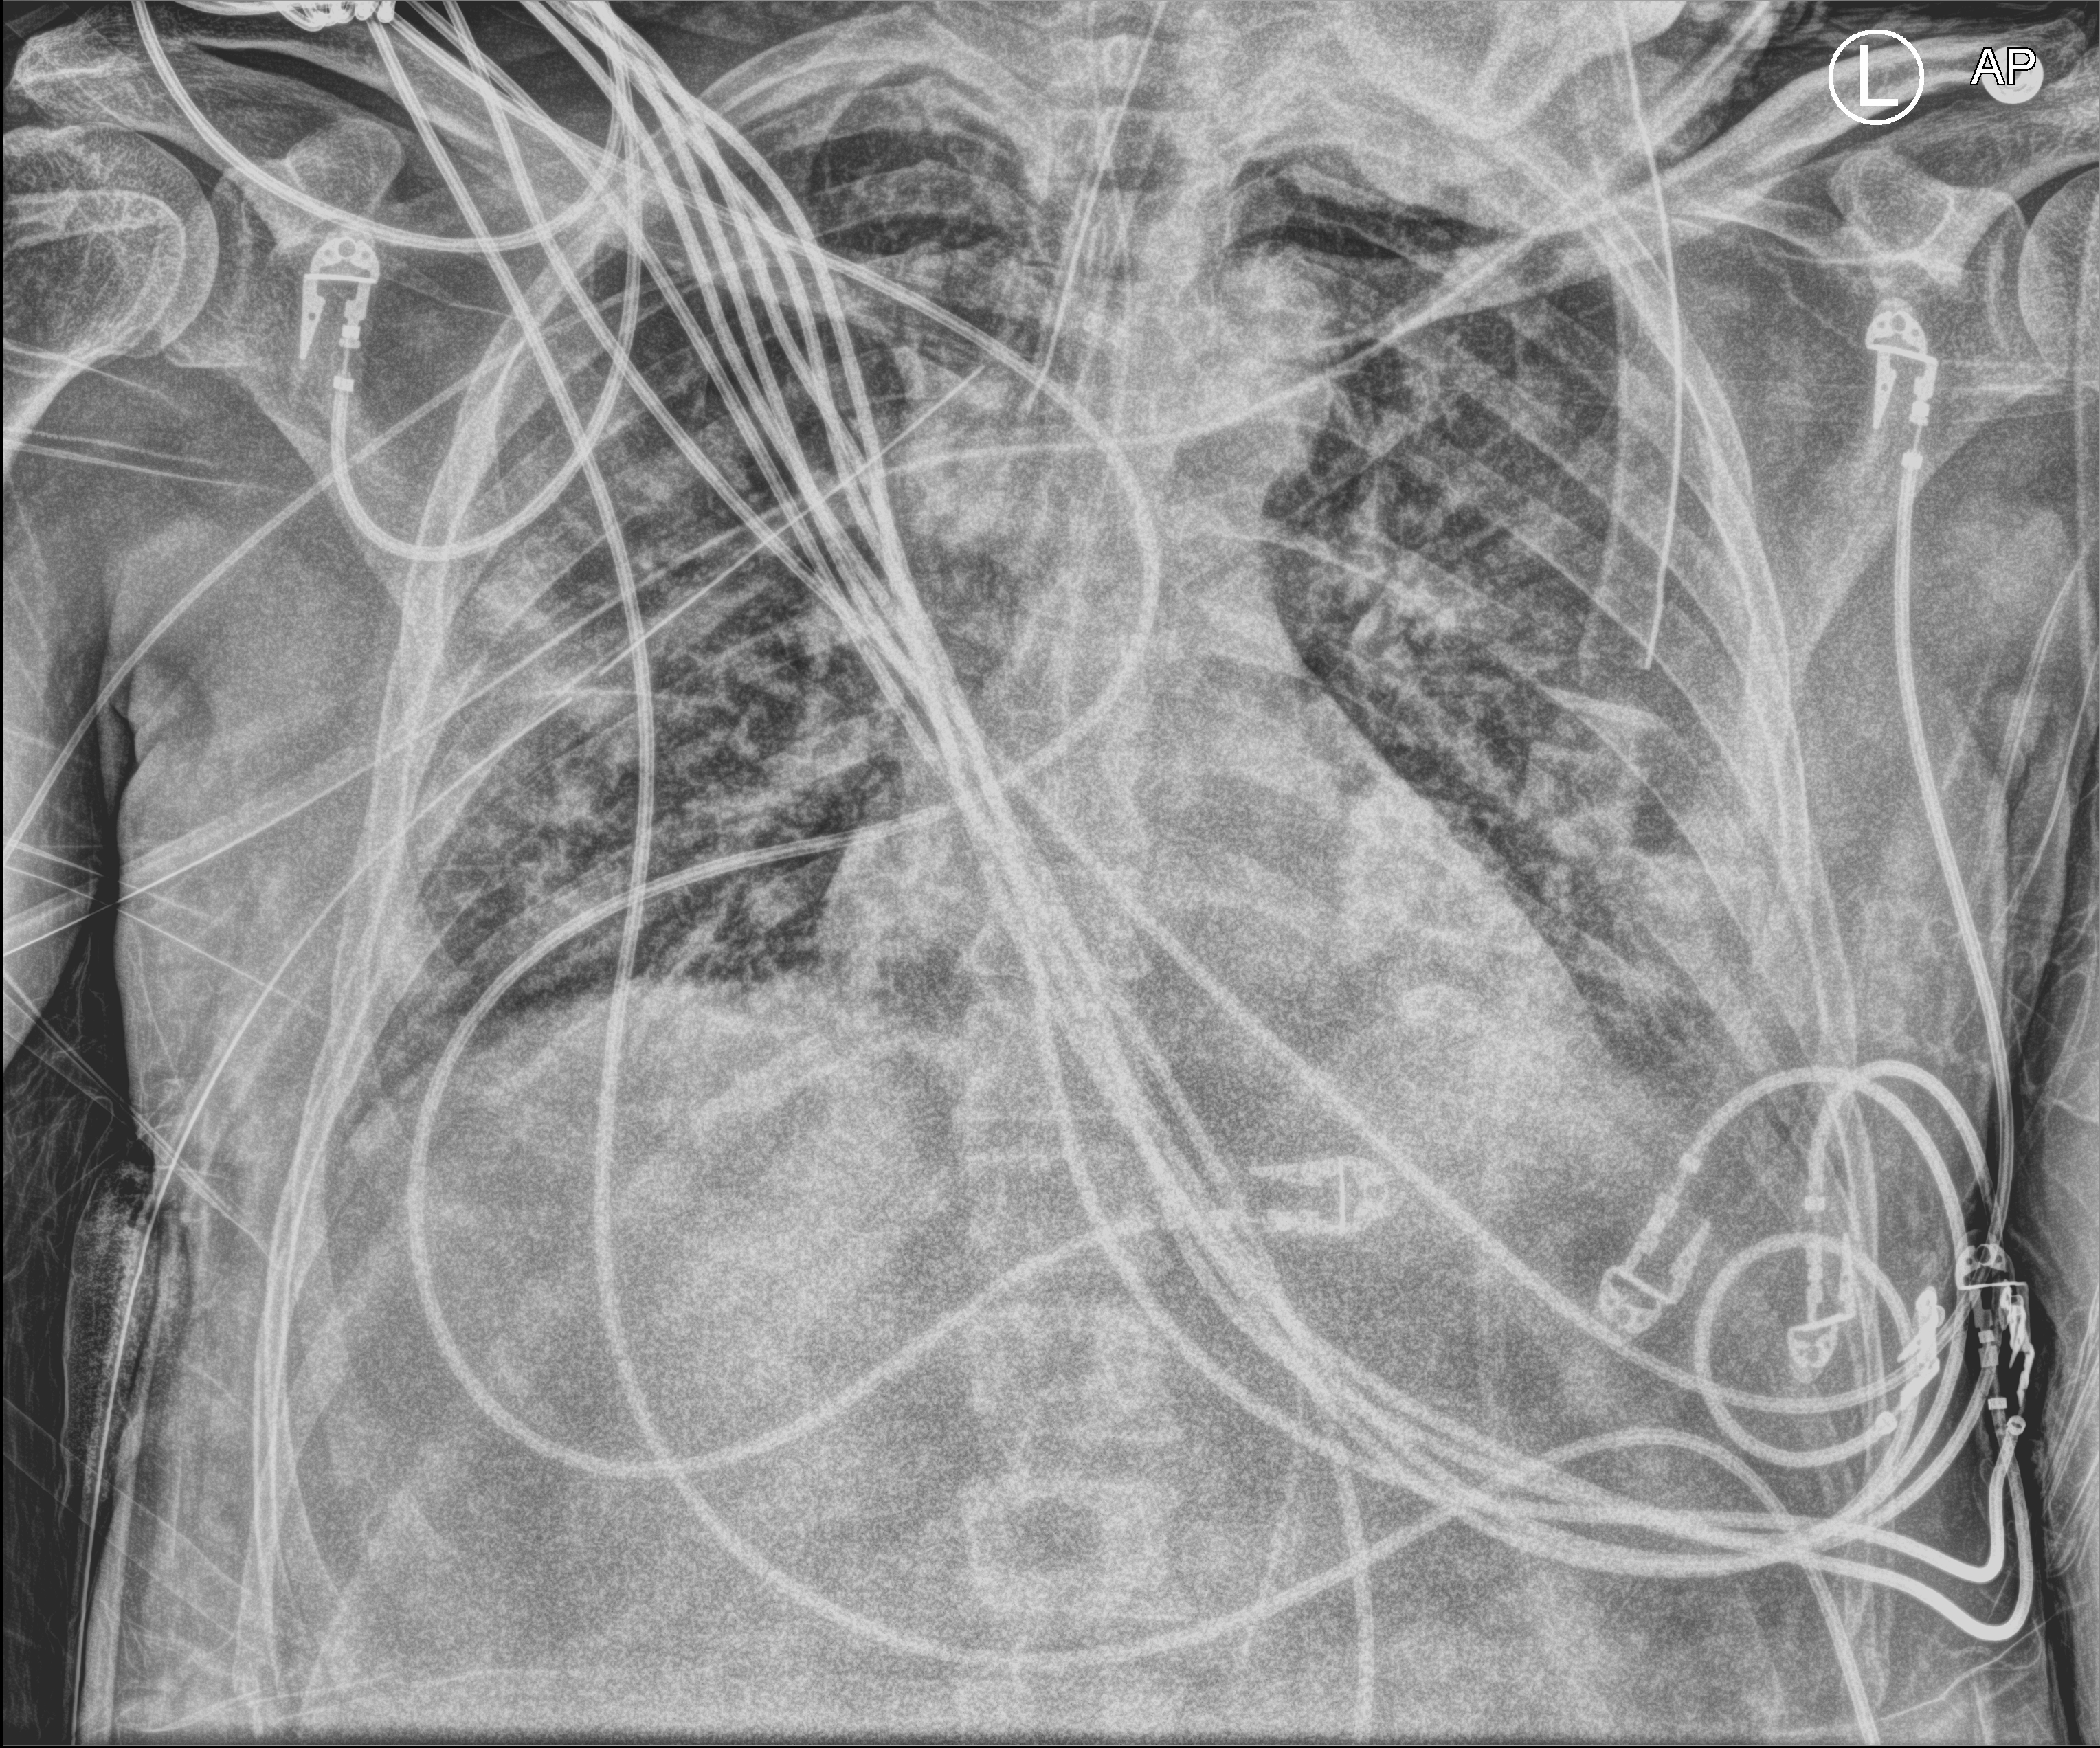
Portable chest radiograph; anteroposterior (AP) projection. Patient hospitalised with COVID-19; male, aged 18–59 years.
Admission-level facts for this patient (not findings on this image; timing relative to this image not recorded):
- admitted to intensive care during this hospital stay: yes